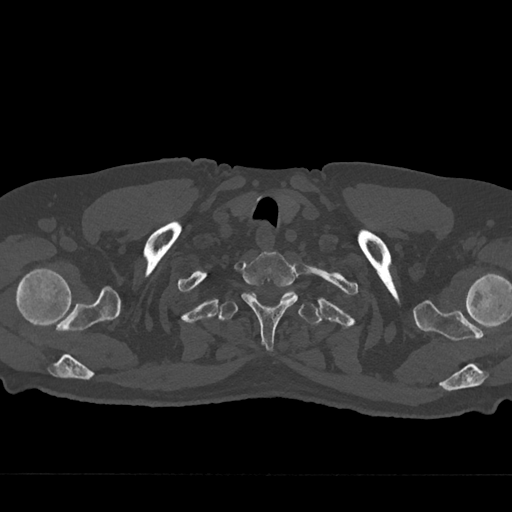
CT including the spine, one axial slice; position 646 of 797 along the scan axis; reconstruction kernel Br40s/3; bone window (W 1800 / L 400 HU); 0.5 mm slice thickness; 512 × 512 image matrix. Patient: male, 75 years. Case-level facts recorded for this patient, not image findings: primary cancer: renal.
Annotated regions visible in this slice (semi-automatic segmentation, software-assisted and operator-edited):
- T1 vertebra: bounding box (x1, y1, x2, y2) in pixels: (241, 252, 298, 351)
- T2 vertebra: (218, 290, 321, 325)